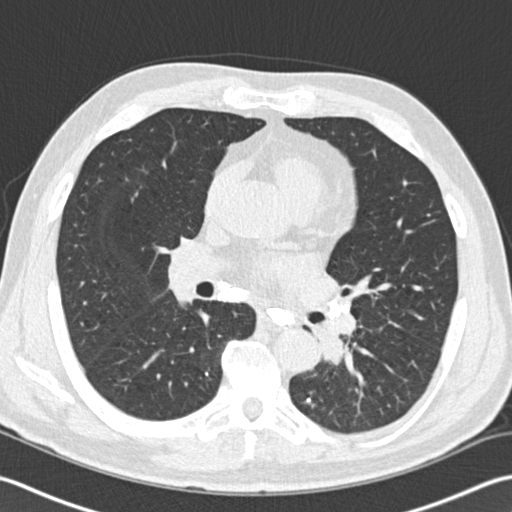
Low-dose screening chest CT, one axial slice. Reconstruction kernel B30f. 120 kVp. Lung window (W 1500 / L -600 HU). 2 mm slice thickness. 512 × 512 image matrix, field of view 350 × 350 mm.
Annotated regions visible in this slice (expert manual segmentation):
- lesion 1 (tumor, lower lobe of left lung): bounding box (x1, y1, x2, y2) in pixels: (312, 320, 347, 363)